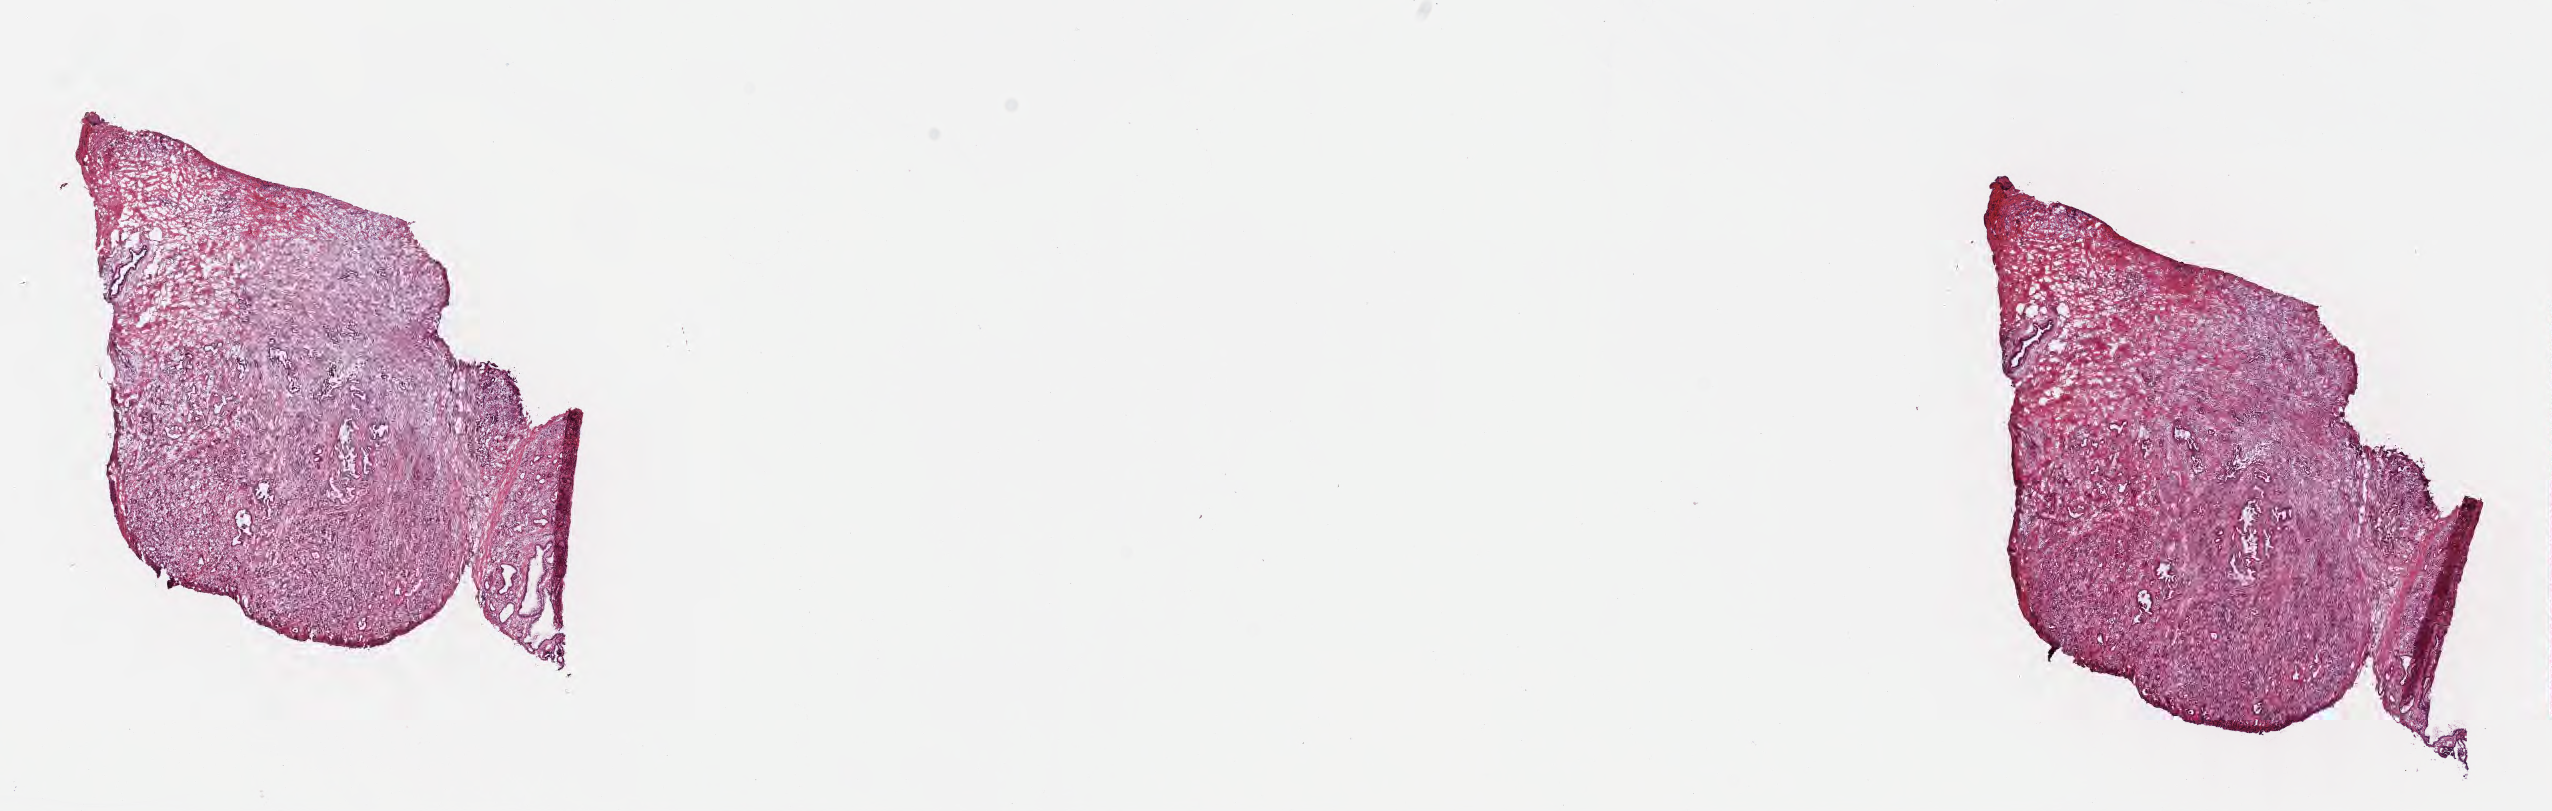
Hematoxylin and eosin (H&E) whole-slide image — whole scanned area (about 20.6 x 6.6 mm) shown as a low-resolution overview; cryosection; primary tumor; site: head of pancreas. Male patient; age at initial diagnosis 69 years. Tumor grade: G2 (moderately differentiated). Pathologist review of this section (percent, as recorded): tumor cells 35%, tumor nuclei 35%, stromal cells 50%, necrosis 0%, normal cells 15%. Inflammatory infiltration, as recorded: lymphocyte infiltration 8%, monocyte infiltration 2%, neutrophil infiltration 2%.
Histologic diagnosis: Infiltrating duct carcinoma, NOS. AJCC pathologic stage: Stage III.